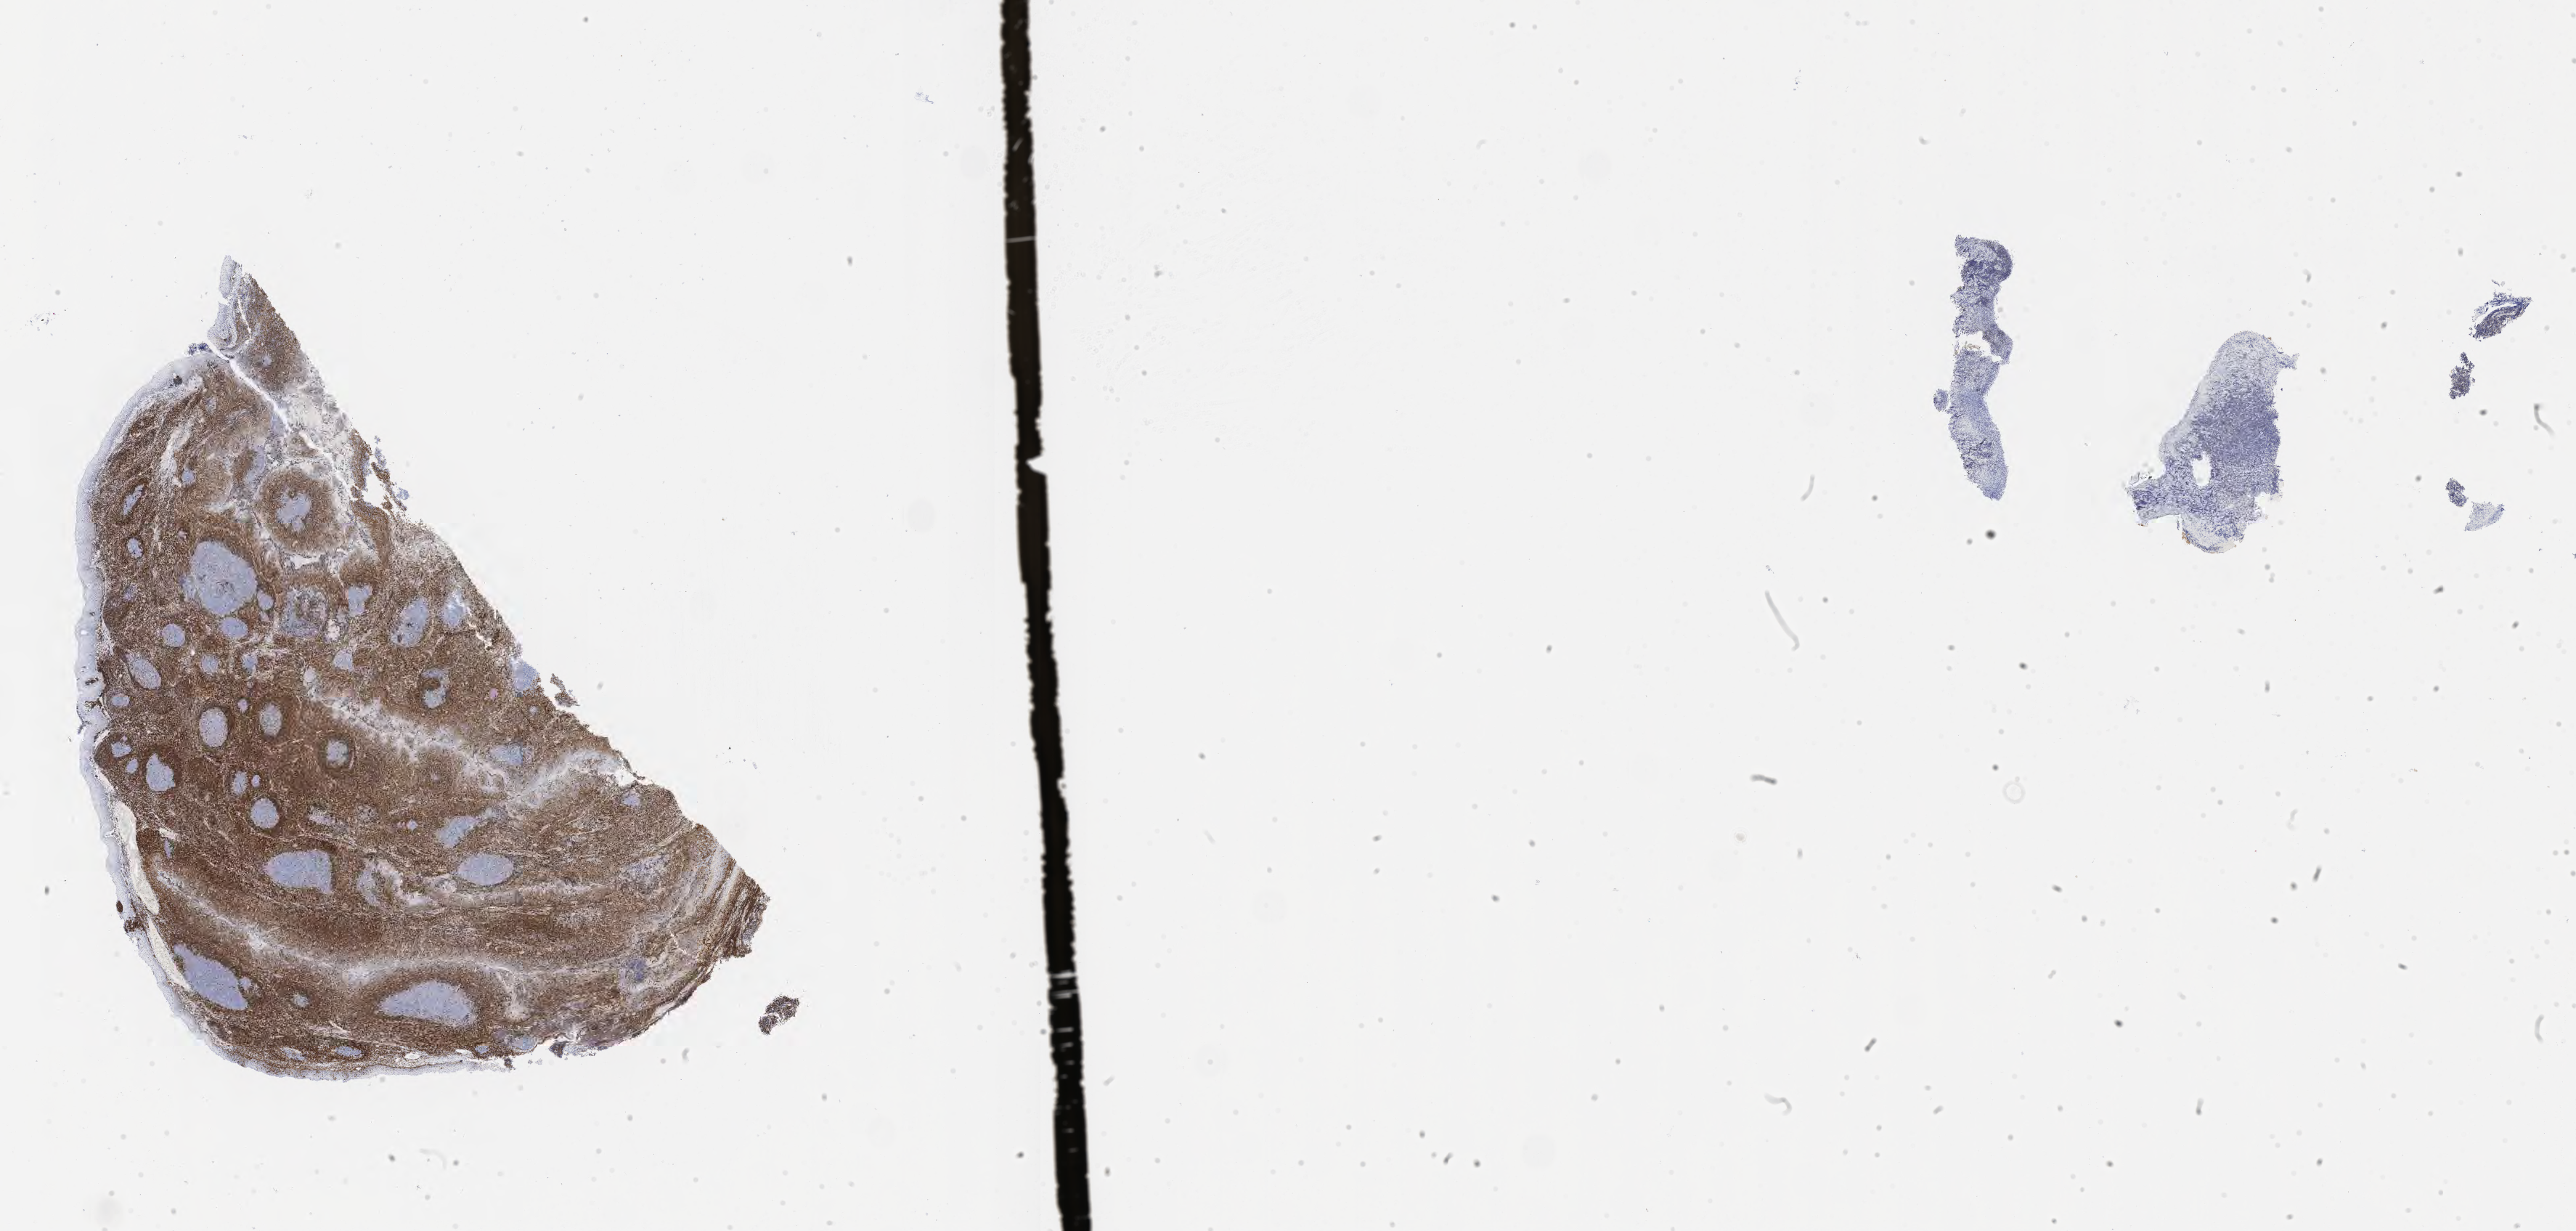
Immunohistochemistry (IHC) whole-slide image stained for BCL2 — a low-resolution overview of the entire scanned area, about 28.7 x 13.7 mm, tumor tissue, site: colon. Patient: male, aged 28.
• diagnosis: Burkitt lymphoma, NOS